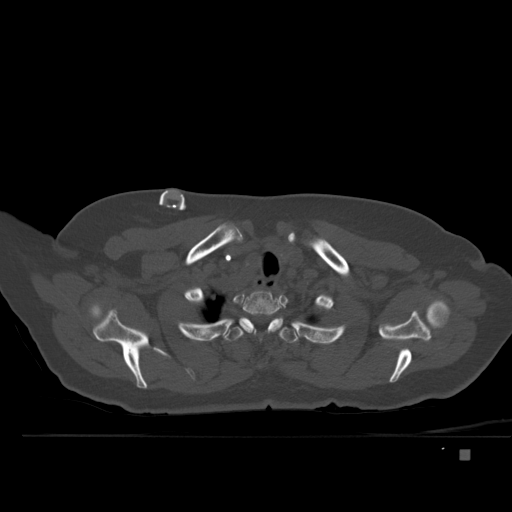
CT including the spine, one axial slice; position 397 of 477 along the scan axis; bone window (W 1800 / L 400 HU); 1.5 mm slice thickness; 512 × 512 image matrix, field of view 422 × 422 mm. Patient: female, 74 years. Case-level facts recorded for this patient, not image findings: primary cancer: colon.
Annotated regions visible in this slice (semi-automatically segmented with operator editing):
- T1 vertebra: bounding box <222,291,283,336> (left, top, right, bottom; pixels)
- T2 vertebra: <198,316,315,343>